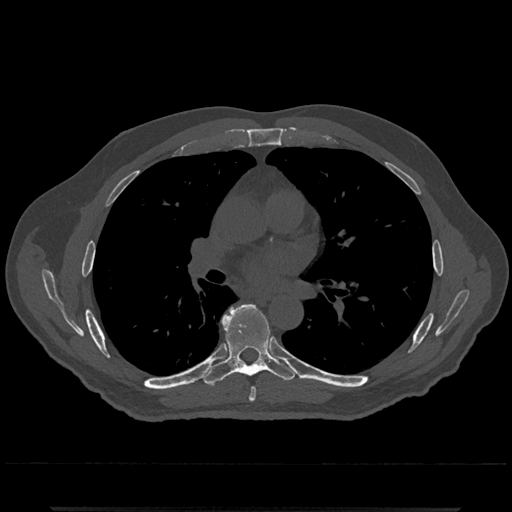
CT including the spine, one axial slice. Position 734 of 797 along the scan axis. 120 kVp. Bone window (W 1800 / L 400 HU). 0.5 mm slice thickness. 512 × 512 image matrix, field of view 393 × 393 mm. Male patient, age 67 years. From the clinical record (not read from this slice): primary cancer: prostate.
Outlined on this slice (semi-automatic segmentation, software-assisted and operator-edited):
- T6 vertebra: bounding box (x1, y1, x2, y2) in pixels: (249, 388, 256, 402)
- T7 vertebra: (203, 304, 296, 386)